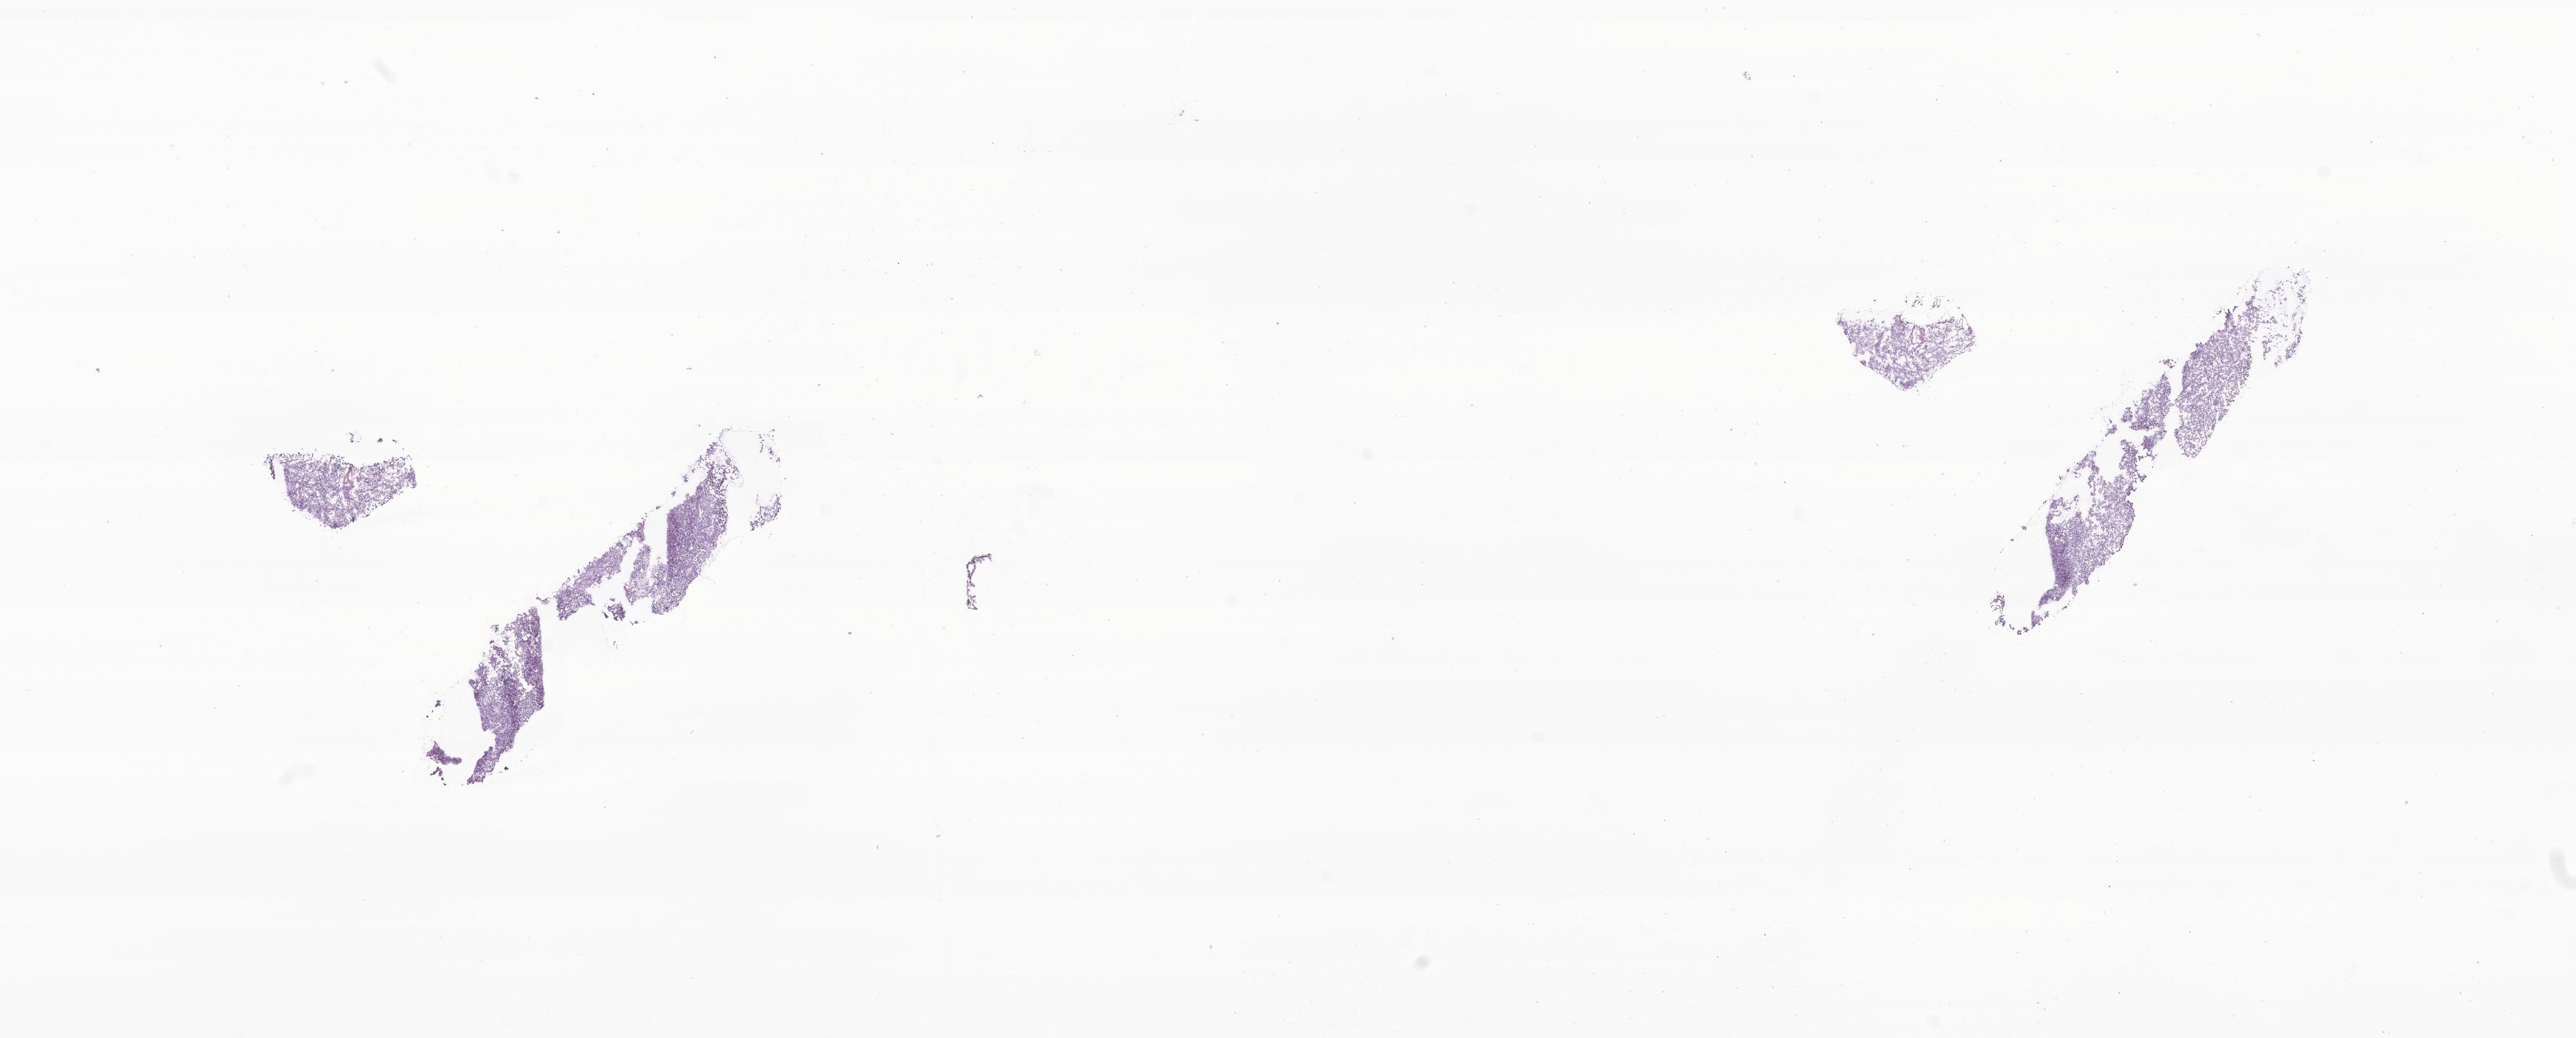
H&E whole-slide image of tumor tissue from the brain, whole scanned area (about 18.8 x 7.6 mm) shown as a low-resolution overview. Frozen section. Female patient, age 37 months (3 years 1 month).
Recorded diagnosis: Meningioma, NOS.